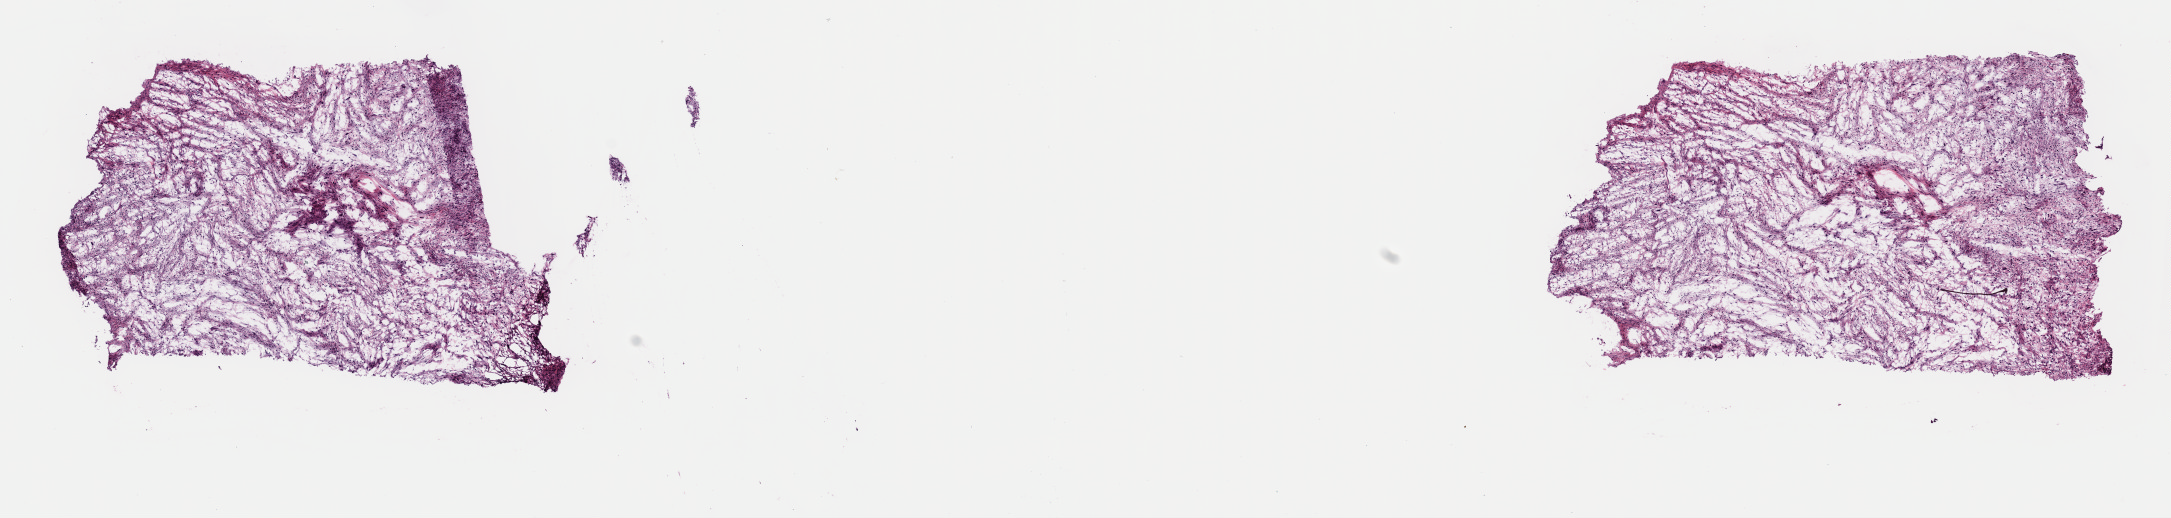
Whole-slide histology image, H&E-stained, whole scanned area (about 17.2 x 4.1 mm, acquisition: 40x scan) shown as a low-resolution overview; frozen section; sample: primary tumour, connective, subcutaneous and other soft tissues. Female patient; age at initial diagnosis 31 years.
Pathologic diagnosis: Fibromyxosarcoma.